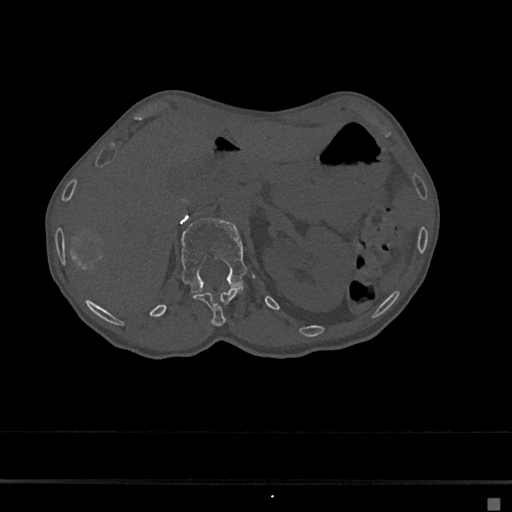
CT including the spine, one axial slice; slice 85 of 797 in the series (ordered by position); bone window (W 1800 / L 400 HU); 512 × 512 image matrix. Female patient, age 68 years. Case-level facts recorded for this patient, not image findings: primary cancer: renal.
Outlined on this slice (semi-automatic segmentation, software-assisted and operator-edited):
- L1 vertebra: bounding box (x1, y1, x2, y2) in pixels: (181, 218, 248, 294)
- T12 vertebra: (192, 287, 243, 327)